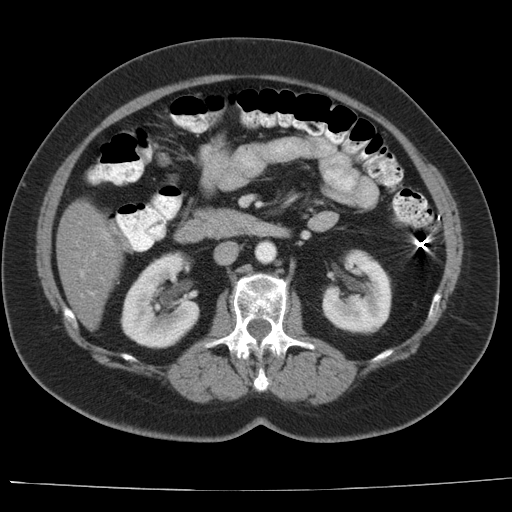
Contrast-enhanced abdominal CT, one axial slice. Slice 8 of 44 in the series (ordered by position). Reconstruction kernel AA-1. 140 kVp. Soft-tissue window (W 400 / L 40 HU). 5 mm slice thickness. 512 × 512 image matrix. Female patient. Case-level facts recorded for this patient, not image findings: diagnosis: colorectal cancer liver metastases, imaged before liver resection.
Outlined on this slice (outlined manually by an expert reader):
- hepatic veins: bounding box (x1, y1, x2, y2) in pixels: (80, 272, 83, 276)
- liver: (58, 201, 122, 329)
- portal vein (with intrahepatic branches): (90, 292, 93, 295)